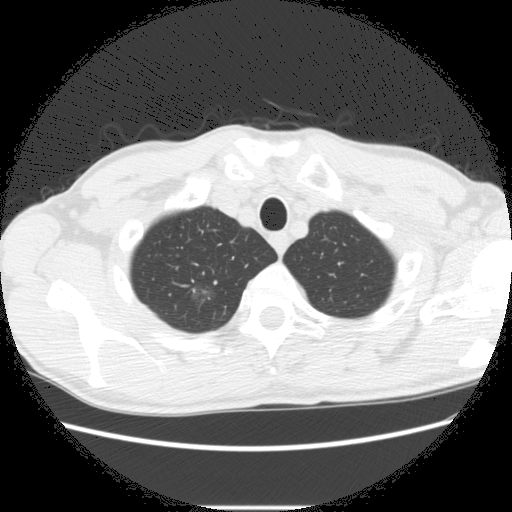
Chest CT (low-dose screening protocol), one axial image. Second annual screen. Lung window (W 1500 / L -600 HU). 2.5 mm slice thickness. 512 × 512 image matrix. Male participant, aged 66 years at enrolment.
• Lesion marked by an expert reader, bounding box [x1, y1, x2, y2] px = [173, 280, 230, 325].
• The screening reader recorded 5 non-calcified nodules or masses ≥4 mm on this exam (right lower lobe, right upper lobe, right upper lobe, right upper lobe, left lower lobe); which of them this box marks is not recorded.
• Later outcome: lung cancer diagnosed 75 days after this screen — adenocarcinoma, NOS, right upper lobe, undifferentiated (G4), stage IA (AJCC 6th edition), 20 mm at pathology.